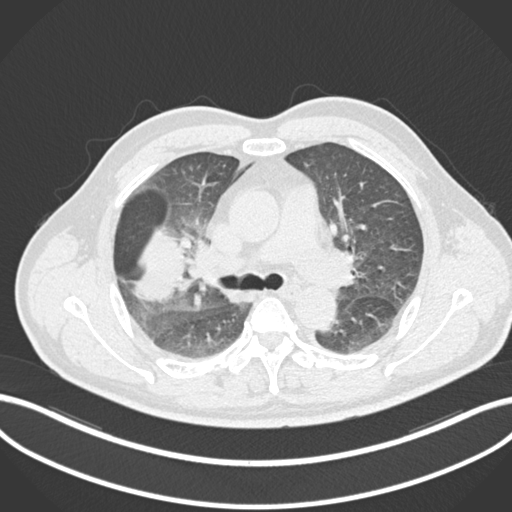
Chest CT, one axial slice. Position 646 of 852 along the scan axis. Lung window (W 1500 / L -600 HU). 1 mm slice thickness. 512 × 512 image matrix, field of view 400 × 400 mm. Patient: male, 55 years. Case-level facts recorded for this patient, not image findings: clinical TNM (as recorded): T3 N2 M1.
Outlined on this slice (rectangle marked by the reading radiologist):
- lung tumour (recorded histology: adenocarcinoma): bounding box [x1, y1, x2, y2] px = [130, 221, 186, 303]